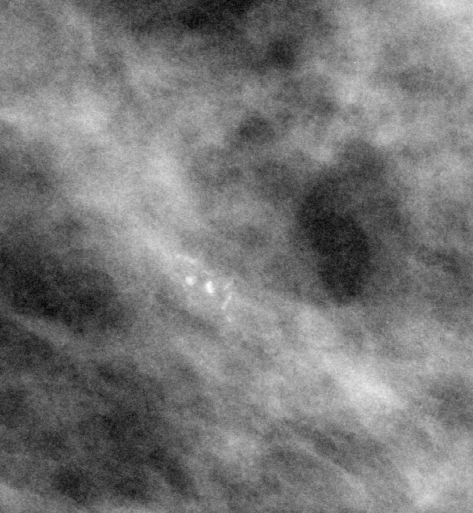
Region of interest cut from a scanned film mammogram (one marked finding), left breast, MLO view, BI-RADS breast density category 2 (scale 1–4).
Finding: calcifications, morphology pleomorphic, distribution clustered; BI-RADS assessment category 5; subtlety rating 5 on a 1 (subtle) to 5 (obvious) scale; pathology result (as recorded, not read from the image): malignant.